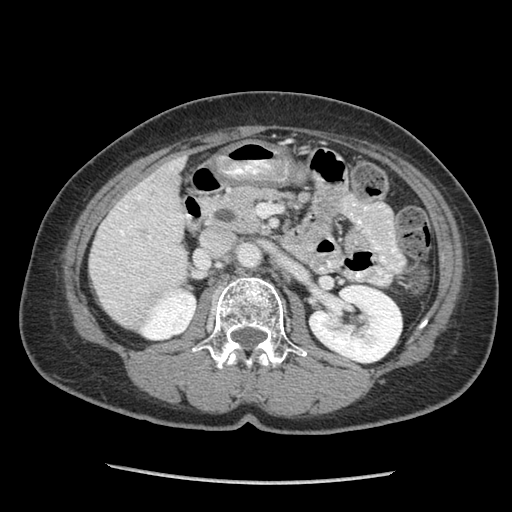
Contrast-enhanced abdominal CT (liver protocol), one axial slice; position 30 of 105 along the scan axis; soft-tissue window (W 400 / L 40 HU); 2.5 mm slice thickness; 512 × 512 image matrix. Case-level facts recorded for this patient, not image findings: diagnosis: hepatocellular carcinoma (patient treated with transarterial chemoembolisation; whether this scan precedes or follows treatment is not stated here); TNM stage (as recorded): Stage-I; Child-Pugh class: A; tumour differentiation: moderately differentiated; tumour nodularity: uninodular.
Outlined on this slice (semi-automatic segmentation, software-assisted and operator-edited):
- liver parenchyma outside the tumour (the mass and vessels are separate outlines, so this box may not span the whole liver): bounding box <90,154,188,324> (left, top, right, bottom; pixels)
- liver vessels: <97,195,182,303>